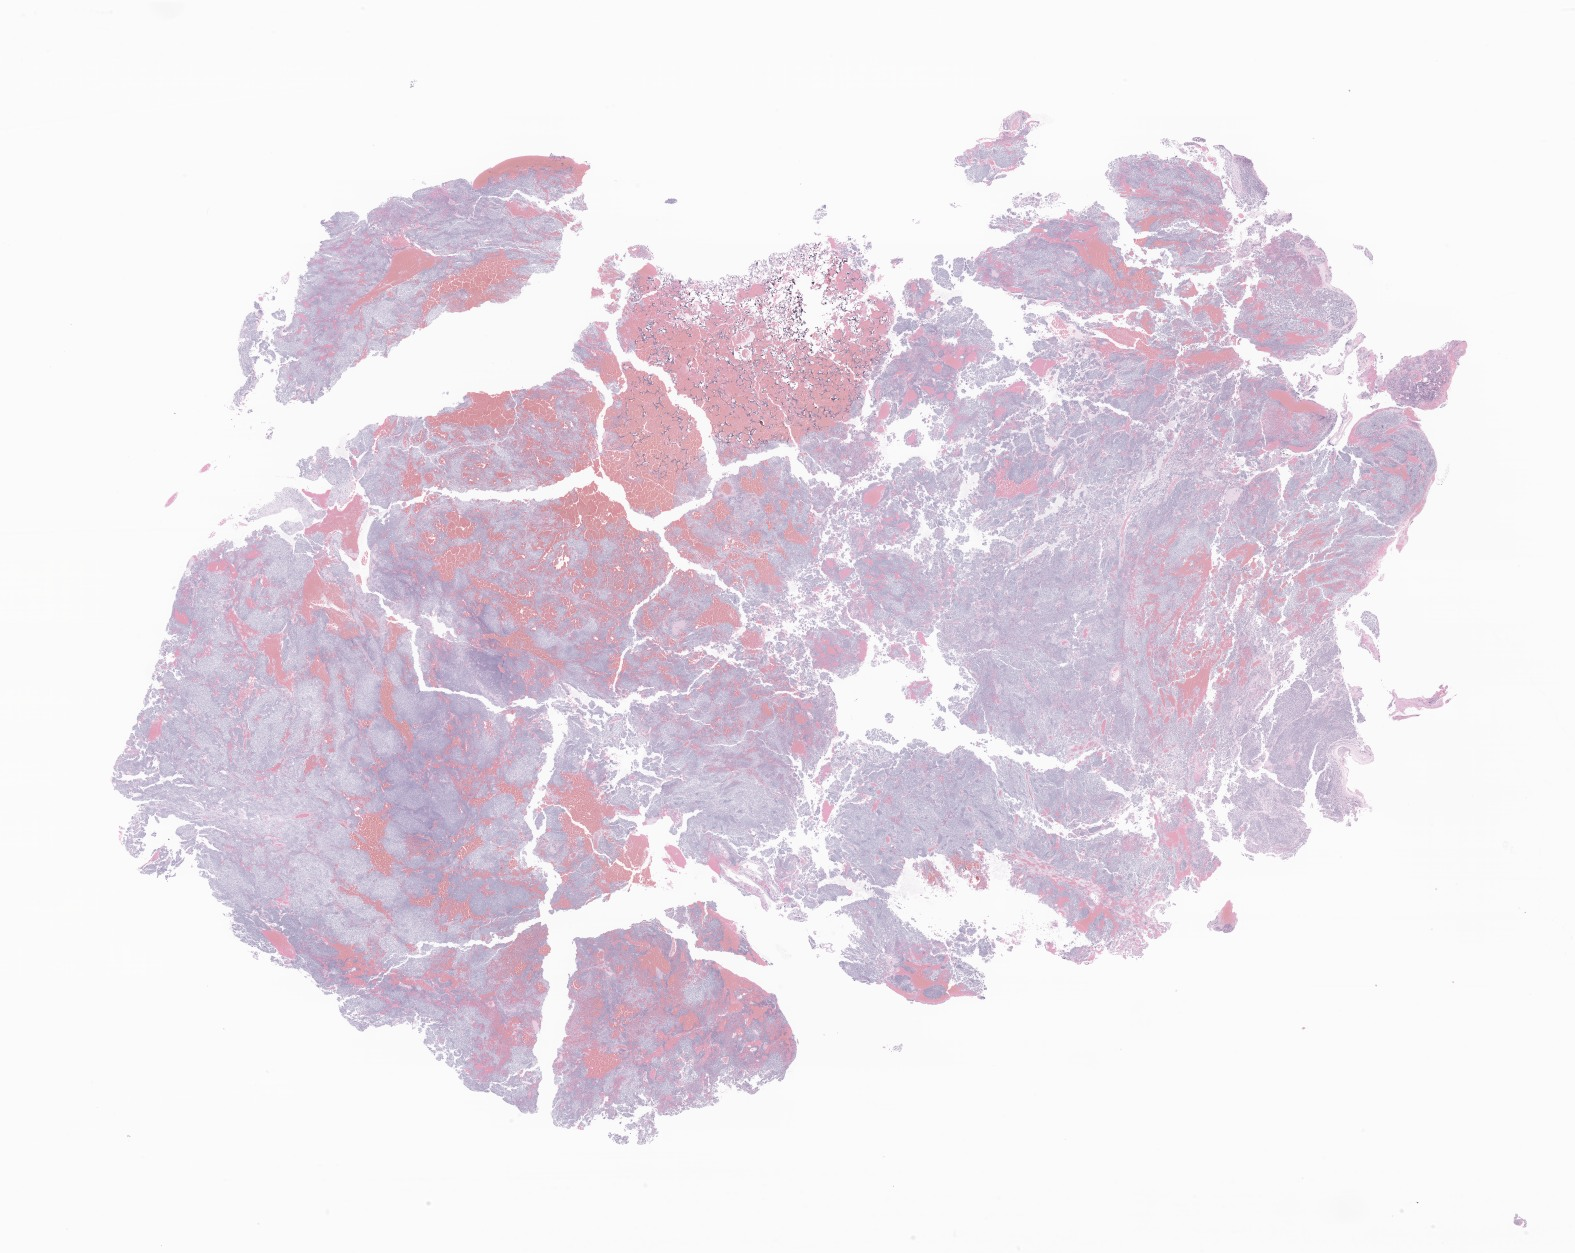
H&E whole-slide image of tumor tissue from the brain, a low-resolution overview of the entire scanned area, about 26.6 x 21.1 mm; formalin-fixed, paraffin-embedded (FFPE) tissue. Patient male; age 47 months (3 years 11 months).
Diagnosis: Neoplasm, malignant.